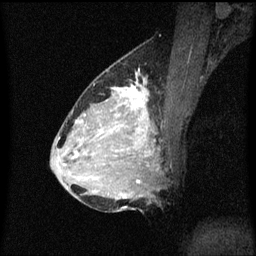
Breast MRI (dynamic contrast-enhanced), one sagittal slice; slice 32 of 60 in the series (ordered by position); dynamic contrast-enhanced series, image 2 of 3 at this slice position (ordered by acquisition); 1.5 T; TE 4.2 ms, TR 8.4 ms; 256 × 256 image matrix. Female patient, age 34 years. From the clinical record (not read from this slice): setting: breast cancer imaged before/during neoadjuvant chemotherapy; receptor status: HR-positive, HER2-negative.
Structures marked on this image (semi-automatic segmentation, software-assisted and operator-edited):
- analysis volume of interest (the breast-tissue region the enhancement analysis was run in; not a lesion): bounding box [x1, y1, x2, y2] px = [69, 70, 169, 209]
- tumour enhancement mask (voxels above the 70 % enhancement threshold inside the analysis volume of interest): [75, 86, 150, 183]